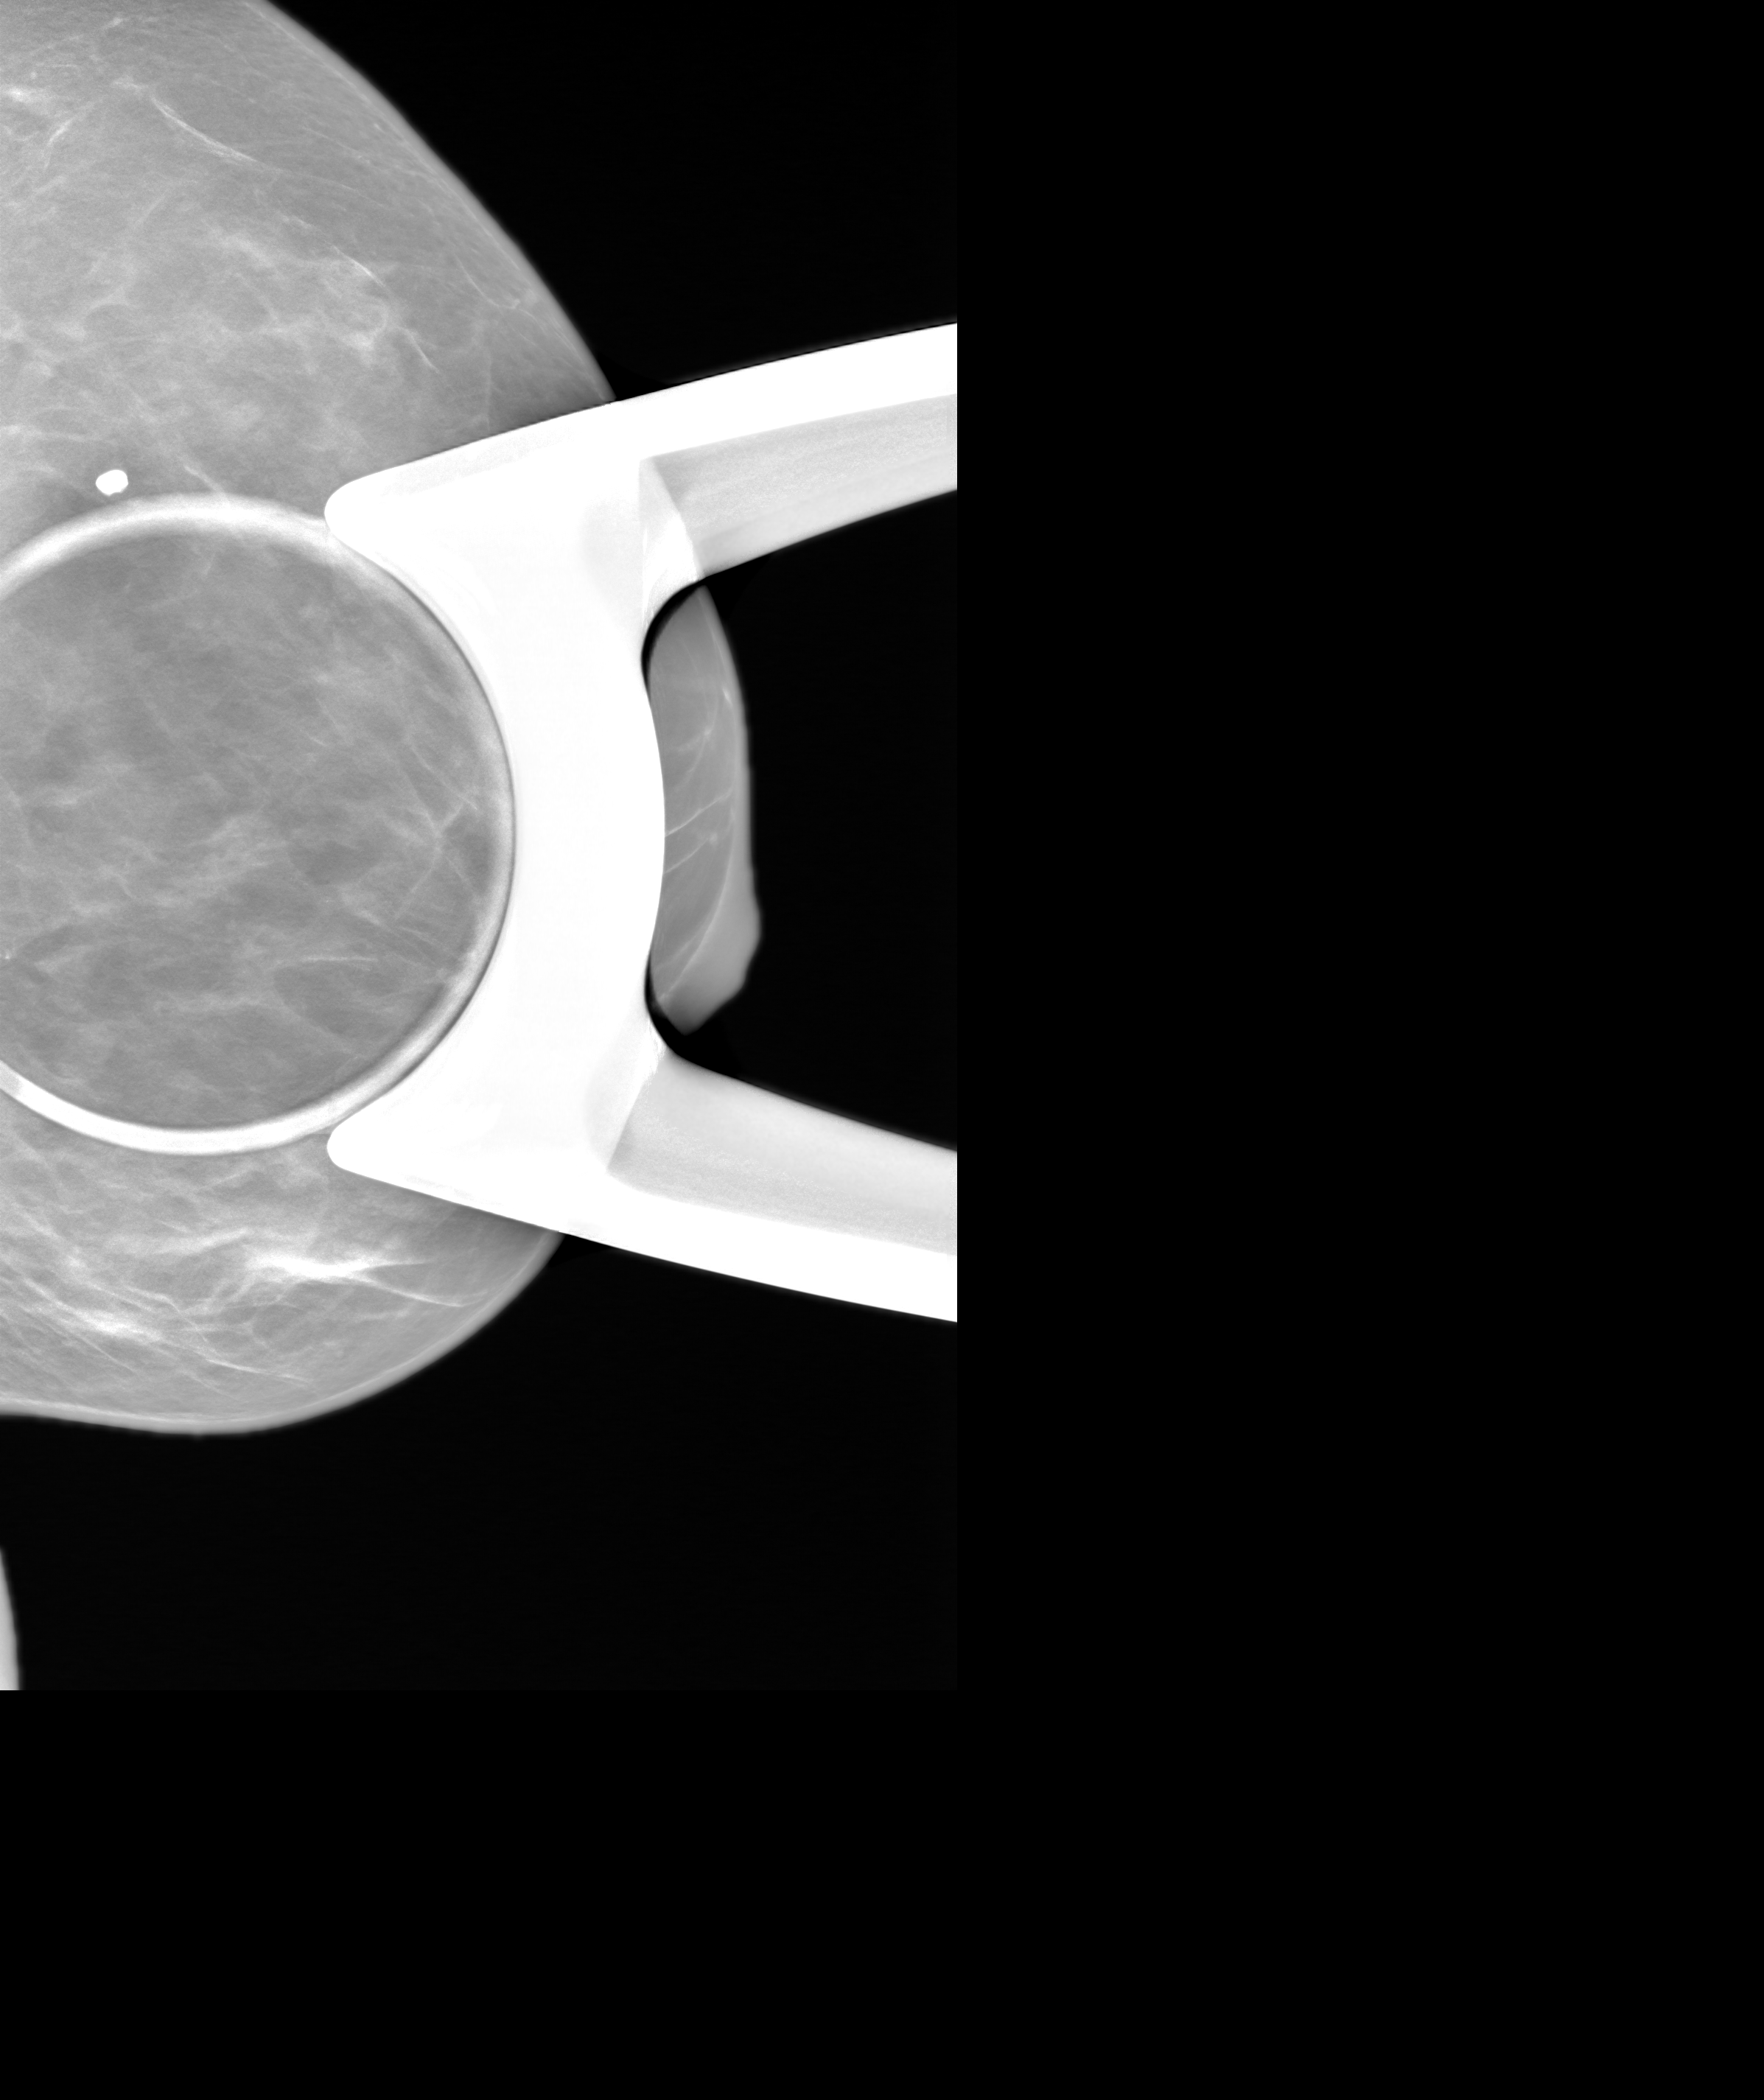
Additional (diagnostic) view. Patient aged 52 years (female).
Image type: synthesized 2-D view from tomosynthesis. Breast: left. Projection: lateromedial (LM) view, spot compression.